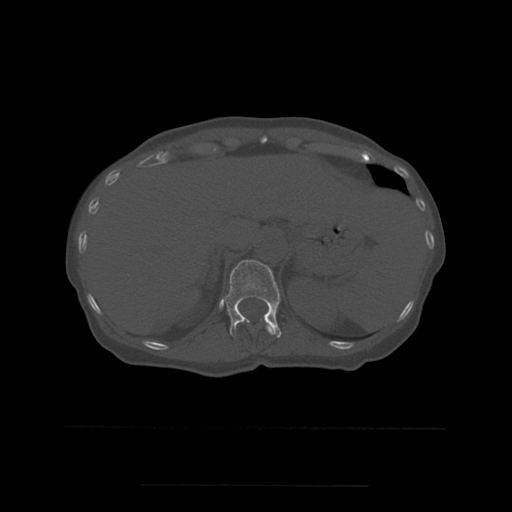
CT including the spine, one axial slice. Slice 265 of 544 in the series (ordered by position). Bone window (W 1800 / L 400 HU). 512 × 512 image matrix. Patient age 58 years. From the clinical record (not read from this slice): primary cancer: lung.
Structures marked on this image (semi-automatic segmentation, software-assisted and operator-edited):
- T11 vertebra: bounding box (x1, y1, x2, y2) in pixels: (238, 320, 276, 335)
- T12 vertebra: (223, 260, 282, 338)